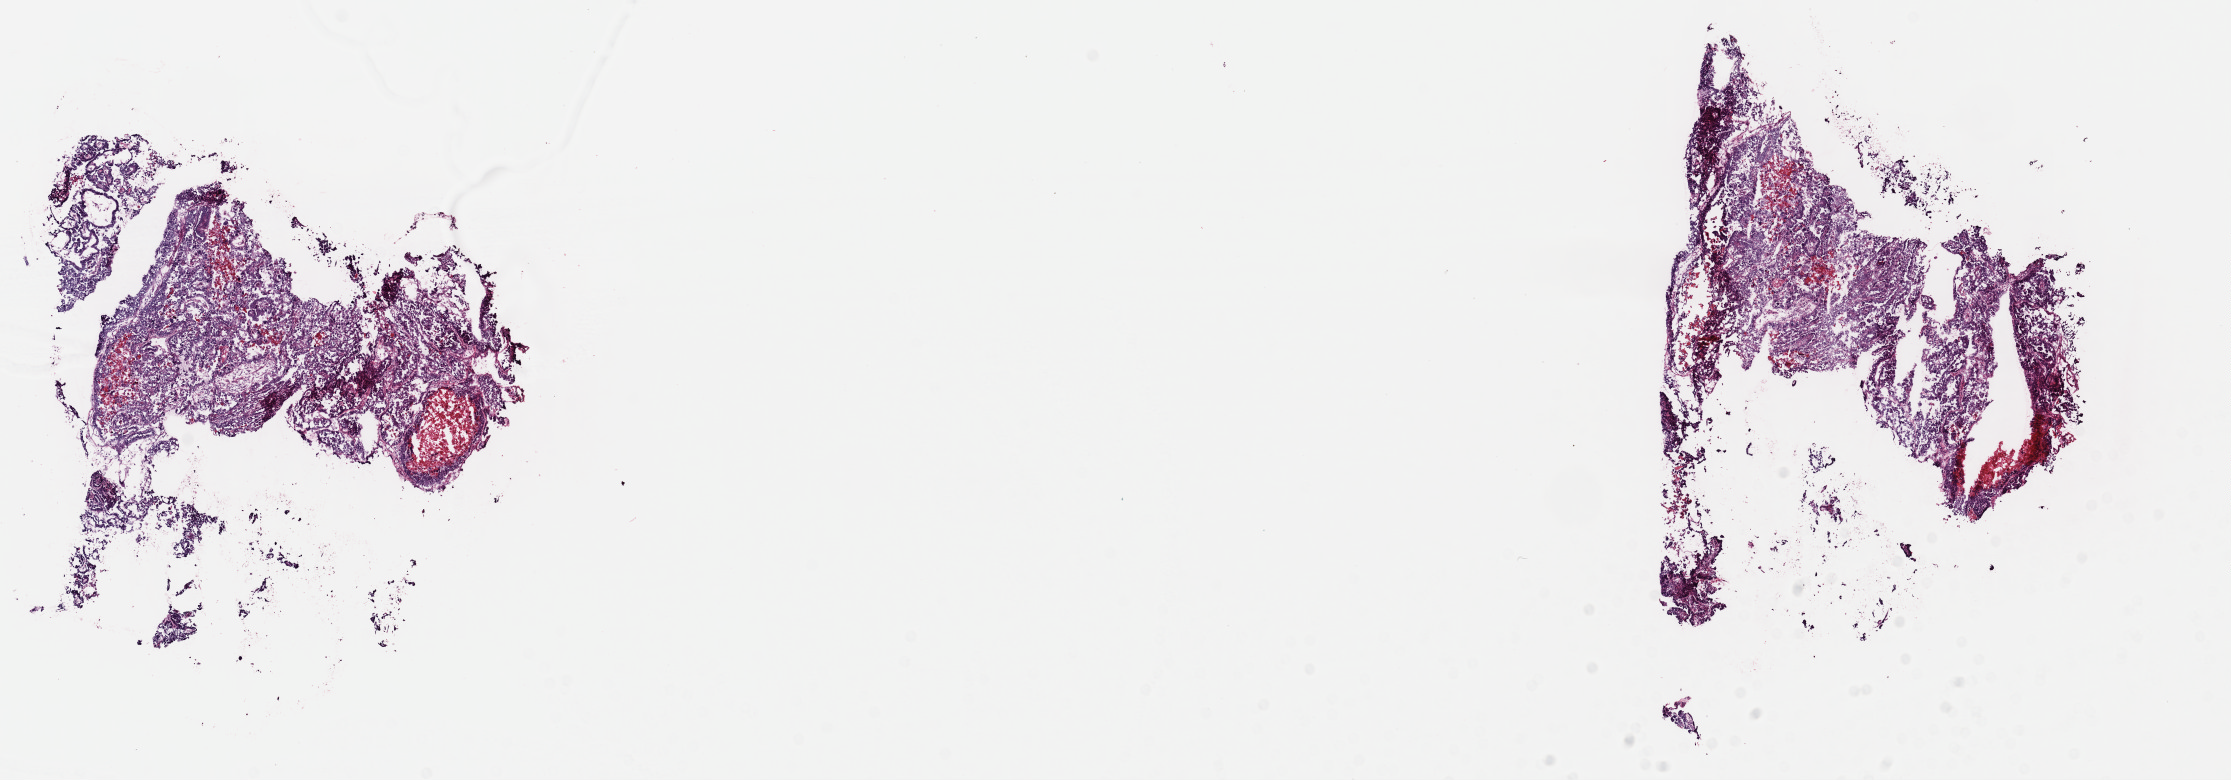
H&E whole-slide image — whole scanned area (about 17.6 x 6.2 mm, from a 40x scan) shown as a low-resolution overview; frozen section from the top of the tissue portion; primary tumour sample from the uterus. Patient: female, age at initial diagnosis 77 years. Histologic grade: G3 (poorly differentiated). Composition of this section per pathologist review: tumour cells 80%, tumour nuclei 80%, normal cells 0%, stromal cells 15%, necrosis 5%. Infiltration values recorded for this section: lymphocyte infiltration 1%, monocyte infiltration 1%, neutrophil infiltration 3%.
* FIGO stage: IA
* pathologic diagnosis: Serous cystadenocarcinoma, NOS (endometrium)